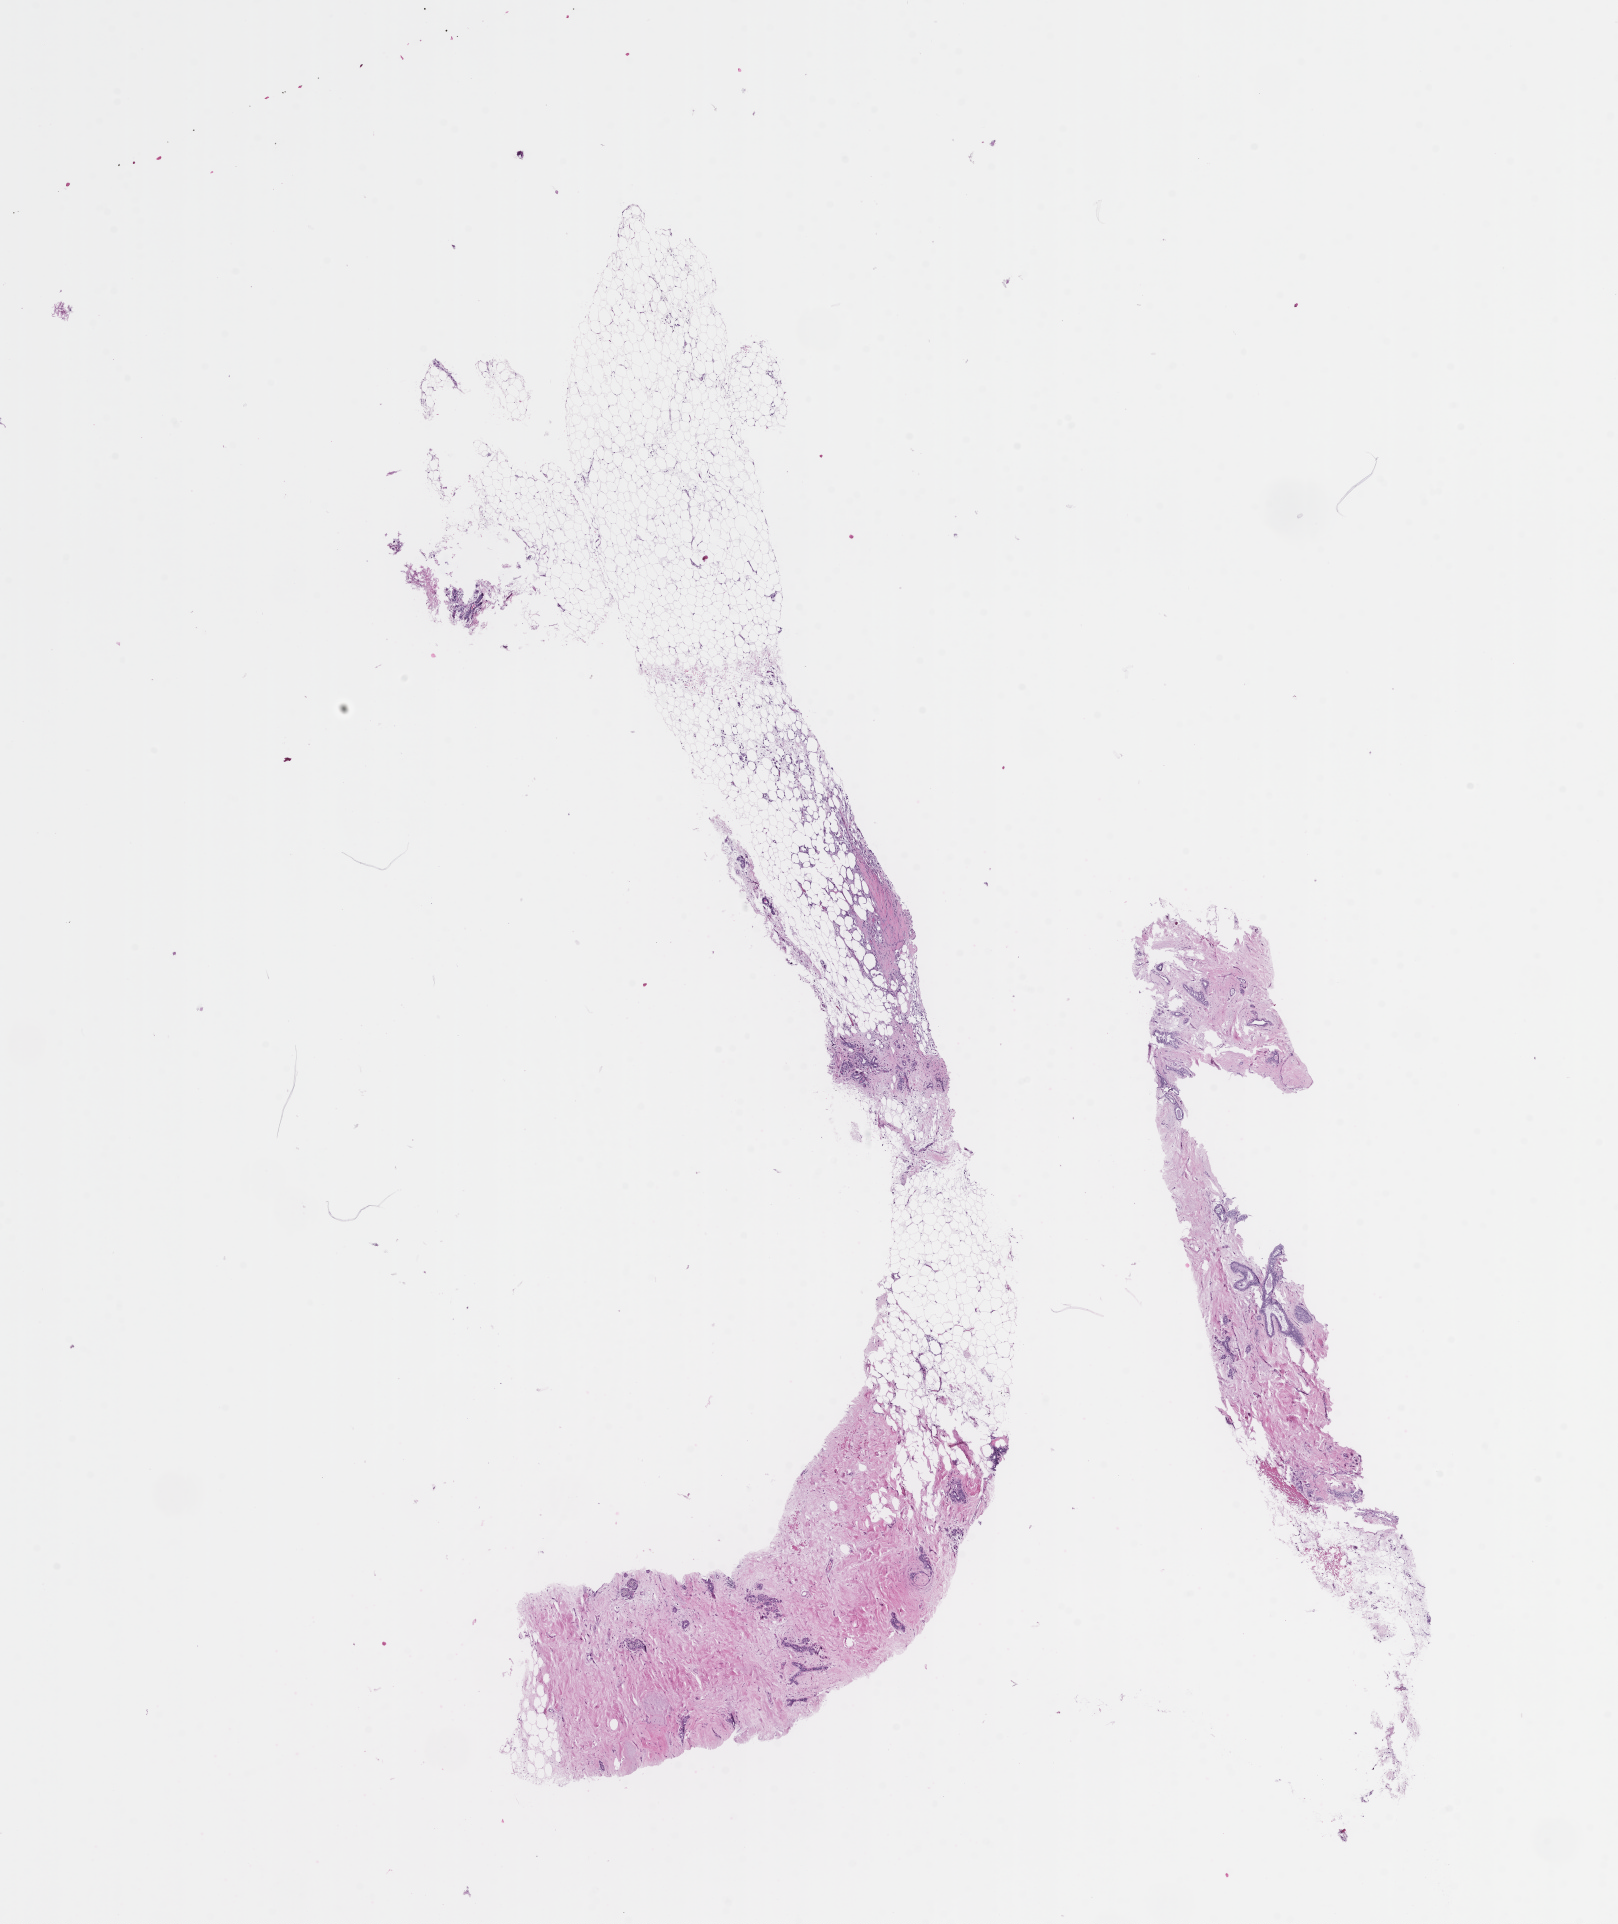
Hematoxylin and eosin (H&E) whole-slide image — low-resolution overview of the scanned area, about 13.1 x 15.5 mm, formalin-fixed, paraffin-embedded (FFPE) tissue, site: breast. Female patient.
This section: primary tumor. Diagnosis: Invasive Breast Carcinoma.